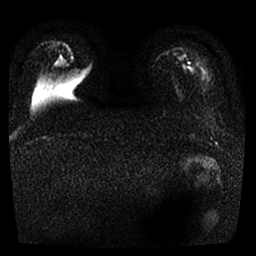
Breast MRI, one axial slice; position 2 of 25 along the scan axis; diffusion-weighted series; image 2 of 4 stored at this slice position (different b-values; order by instance number); 1.5 T; 256 × 256 image matrix, field of view 290 × 290 mm. Female patient.
Structures marked on this image (manually delineated by an expert):
- tumour on diffusion-weighted imaging: box from (x=55, y=60) to (x=68, y=68) px